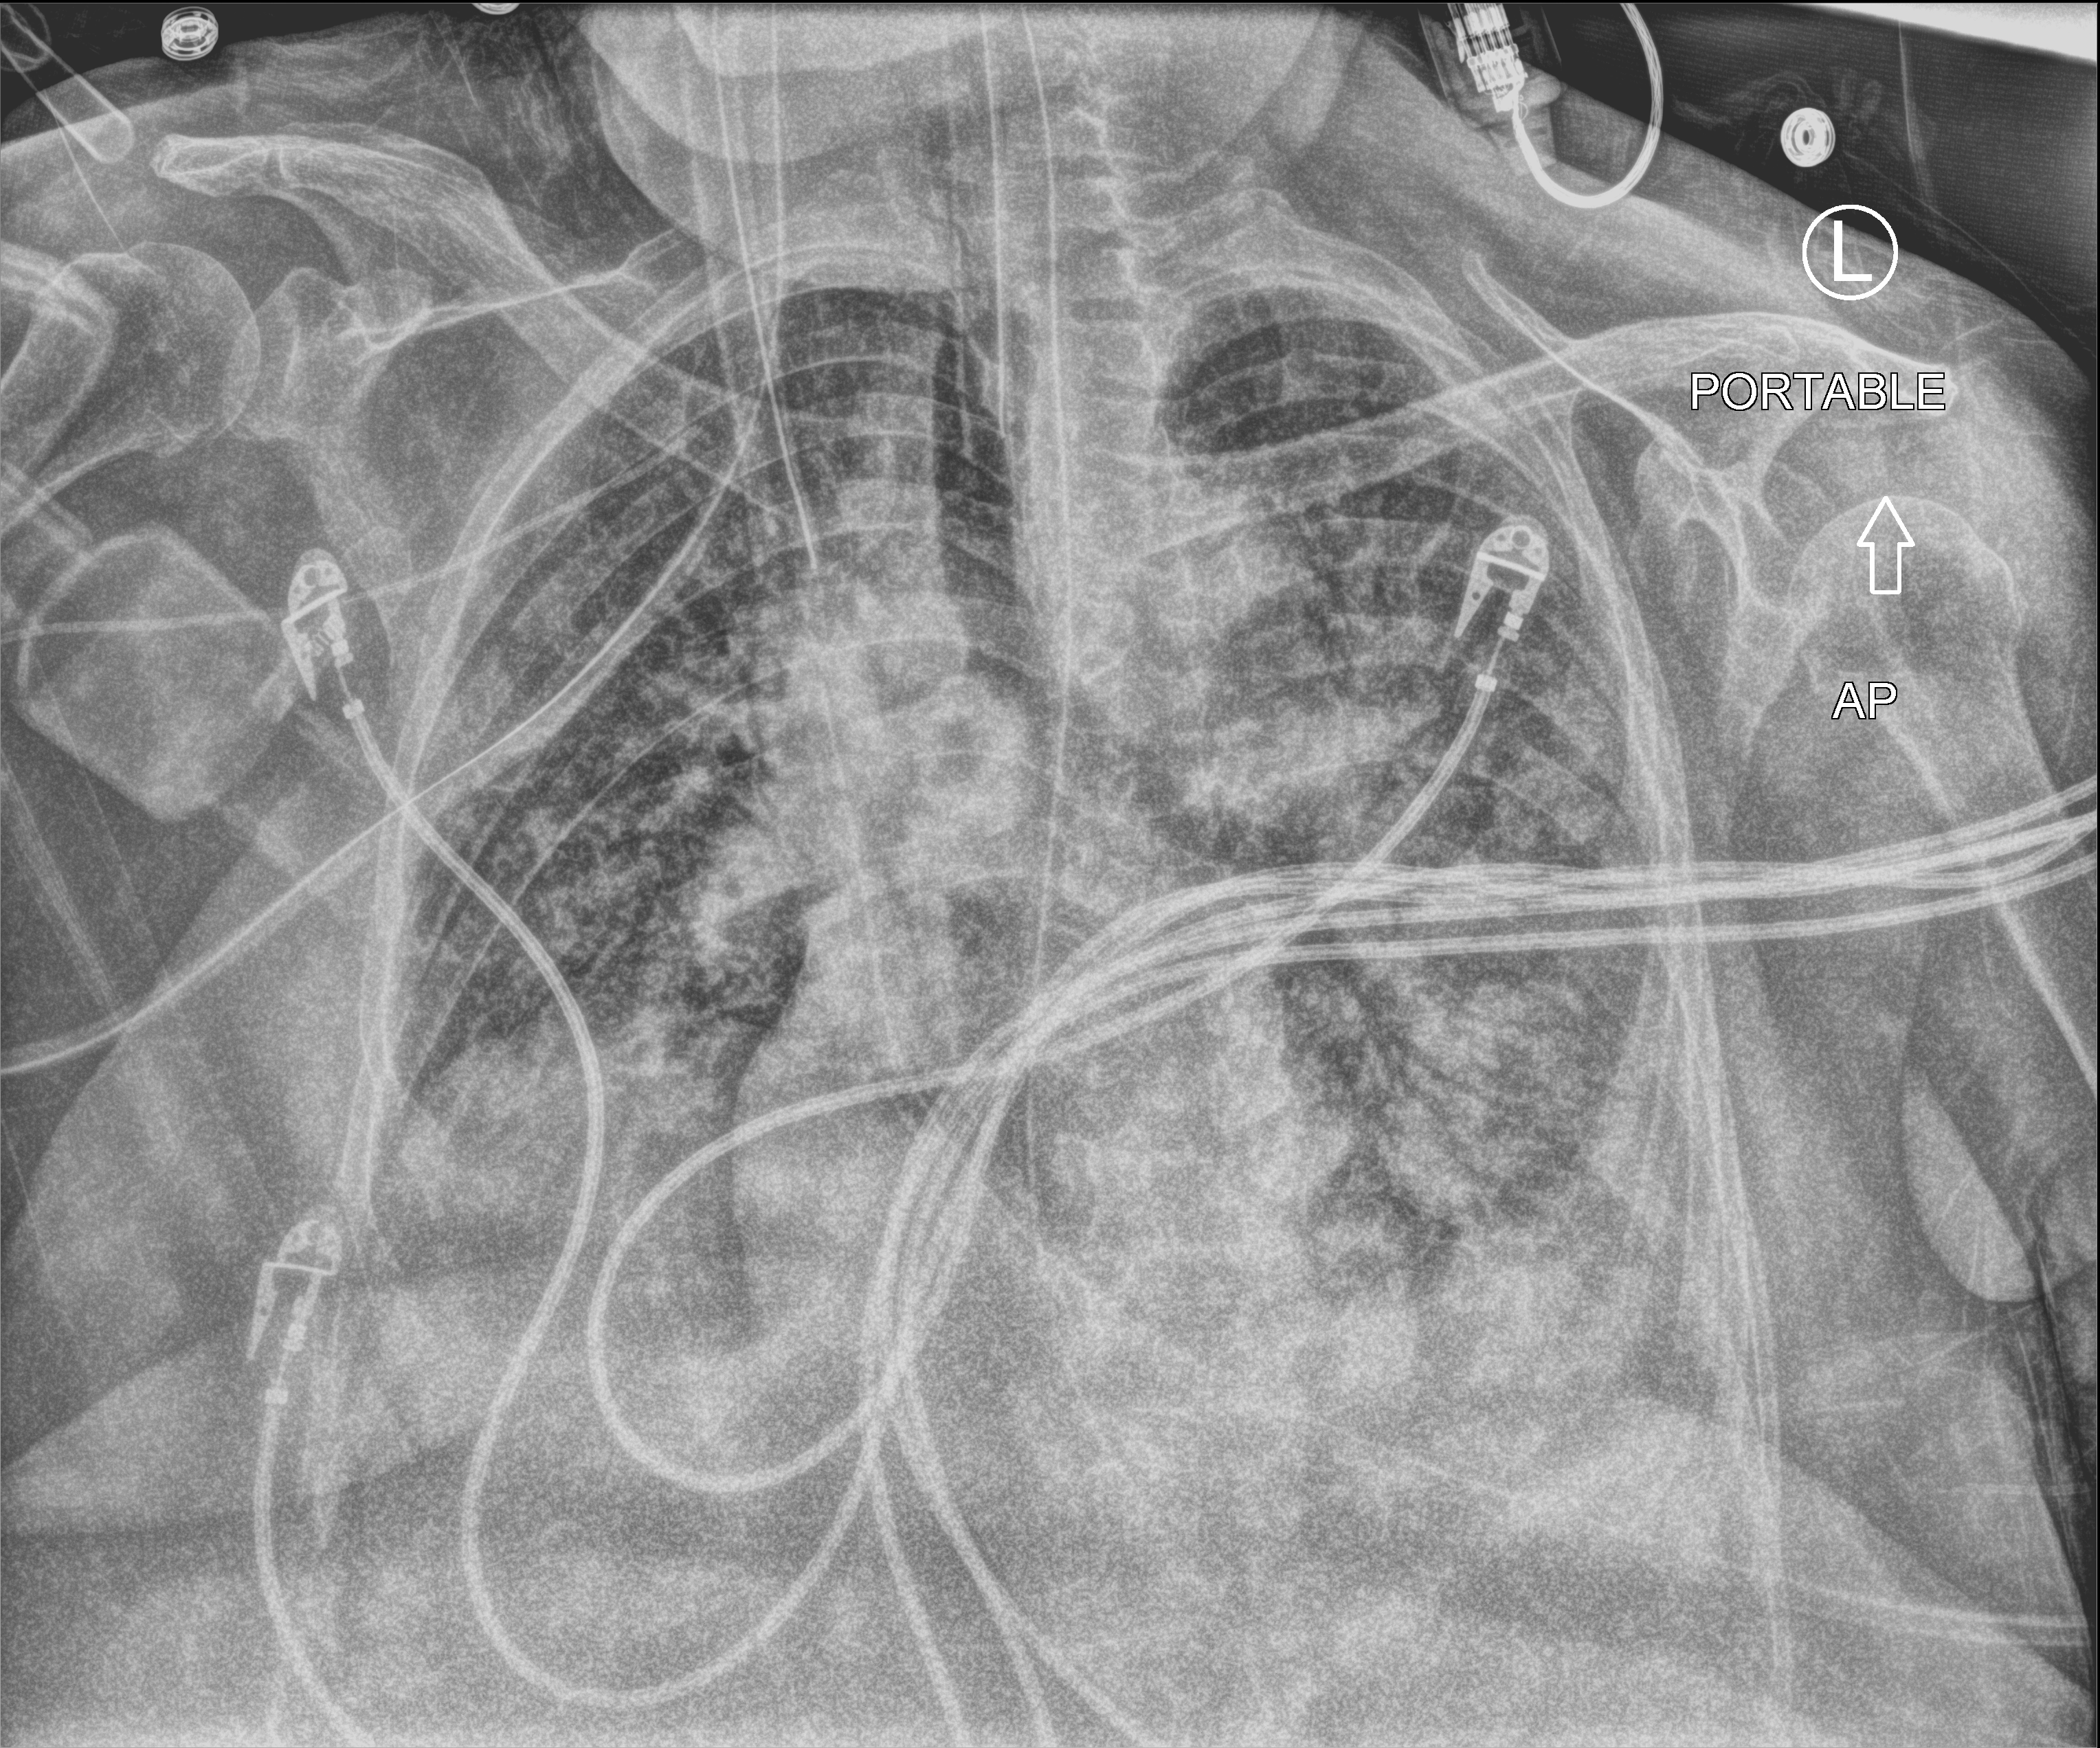
Bedside chest radiograph (computed radiography); anteroposterior (AP) projection. Female patient hospitalised with COVID-19, age 60–74 years.
Hospital-stay facts (about this admission, not read from this image; timing relative to this image not recorded): admitted to intensive care during this hospital stay: yes; mechanically ventilated during this hospital stay: yes; chronic kidney disease (admission record): no.